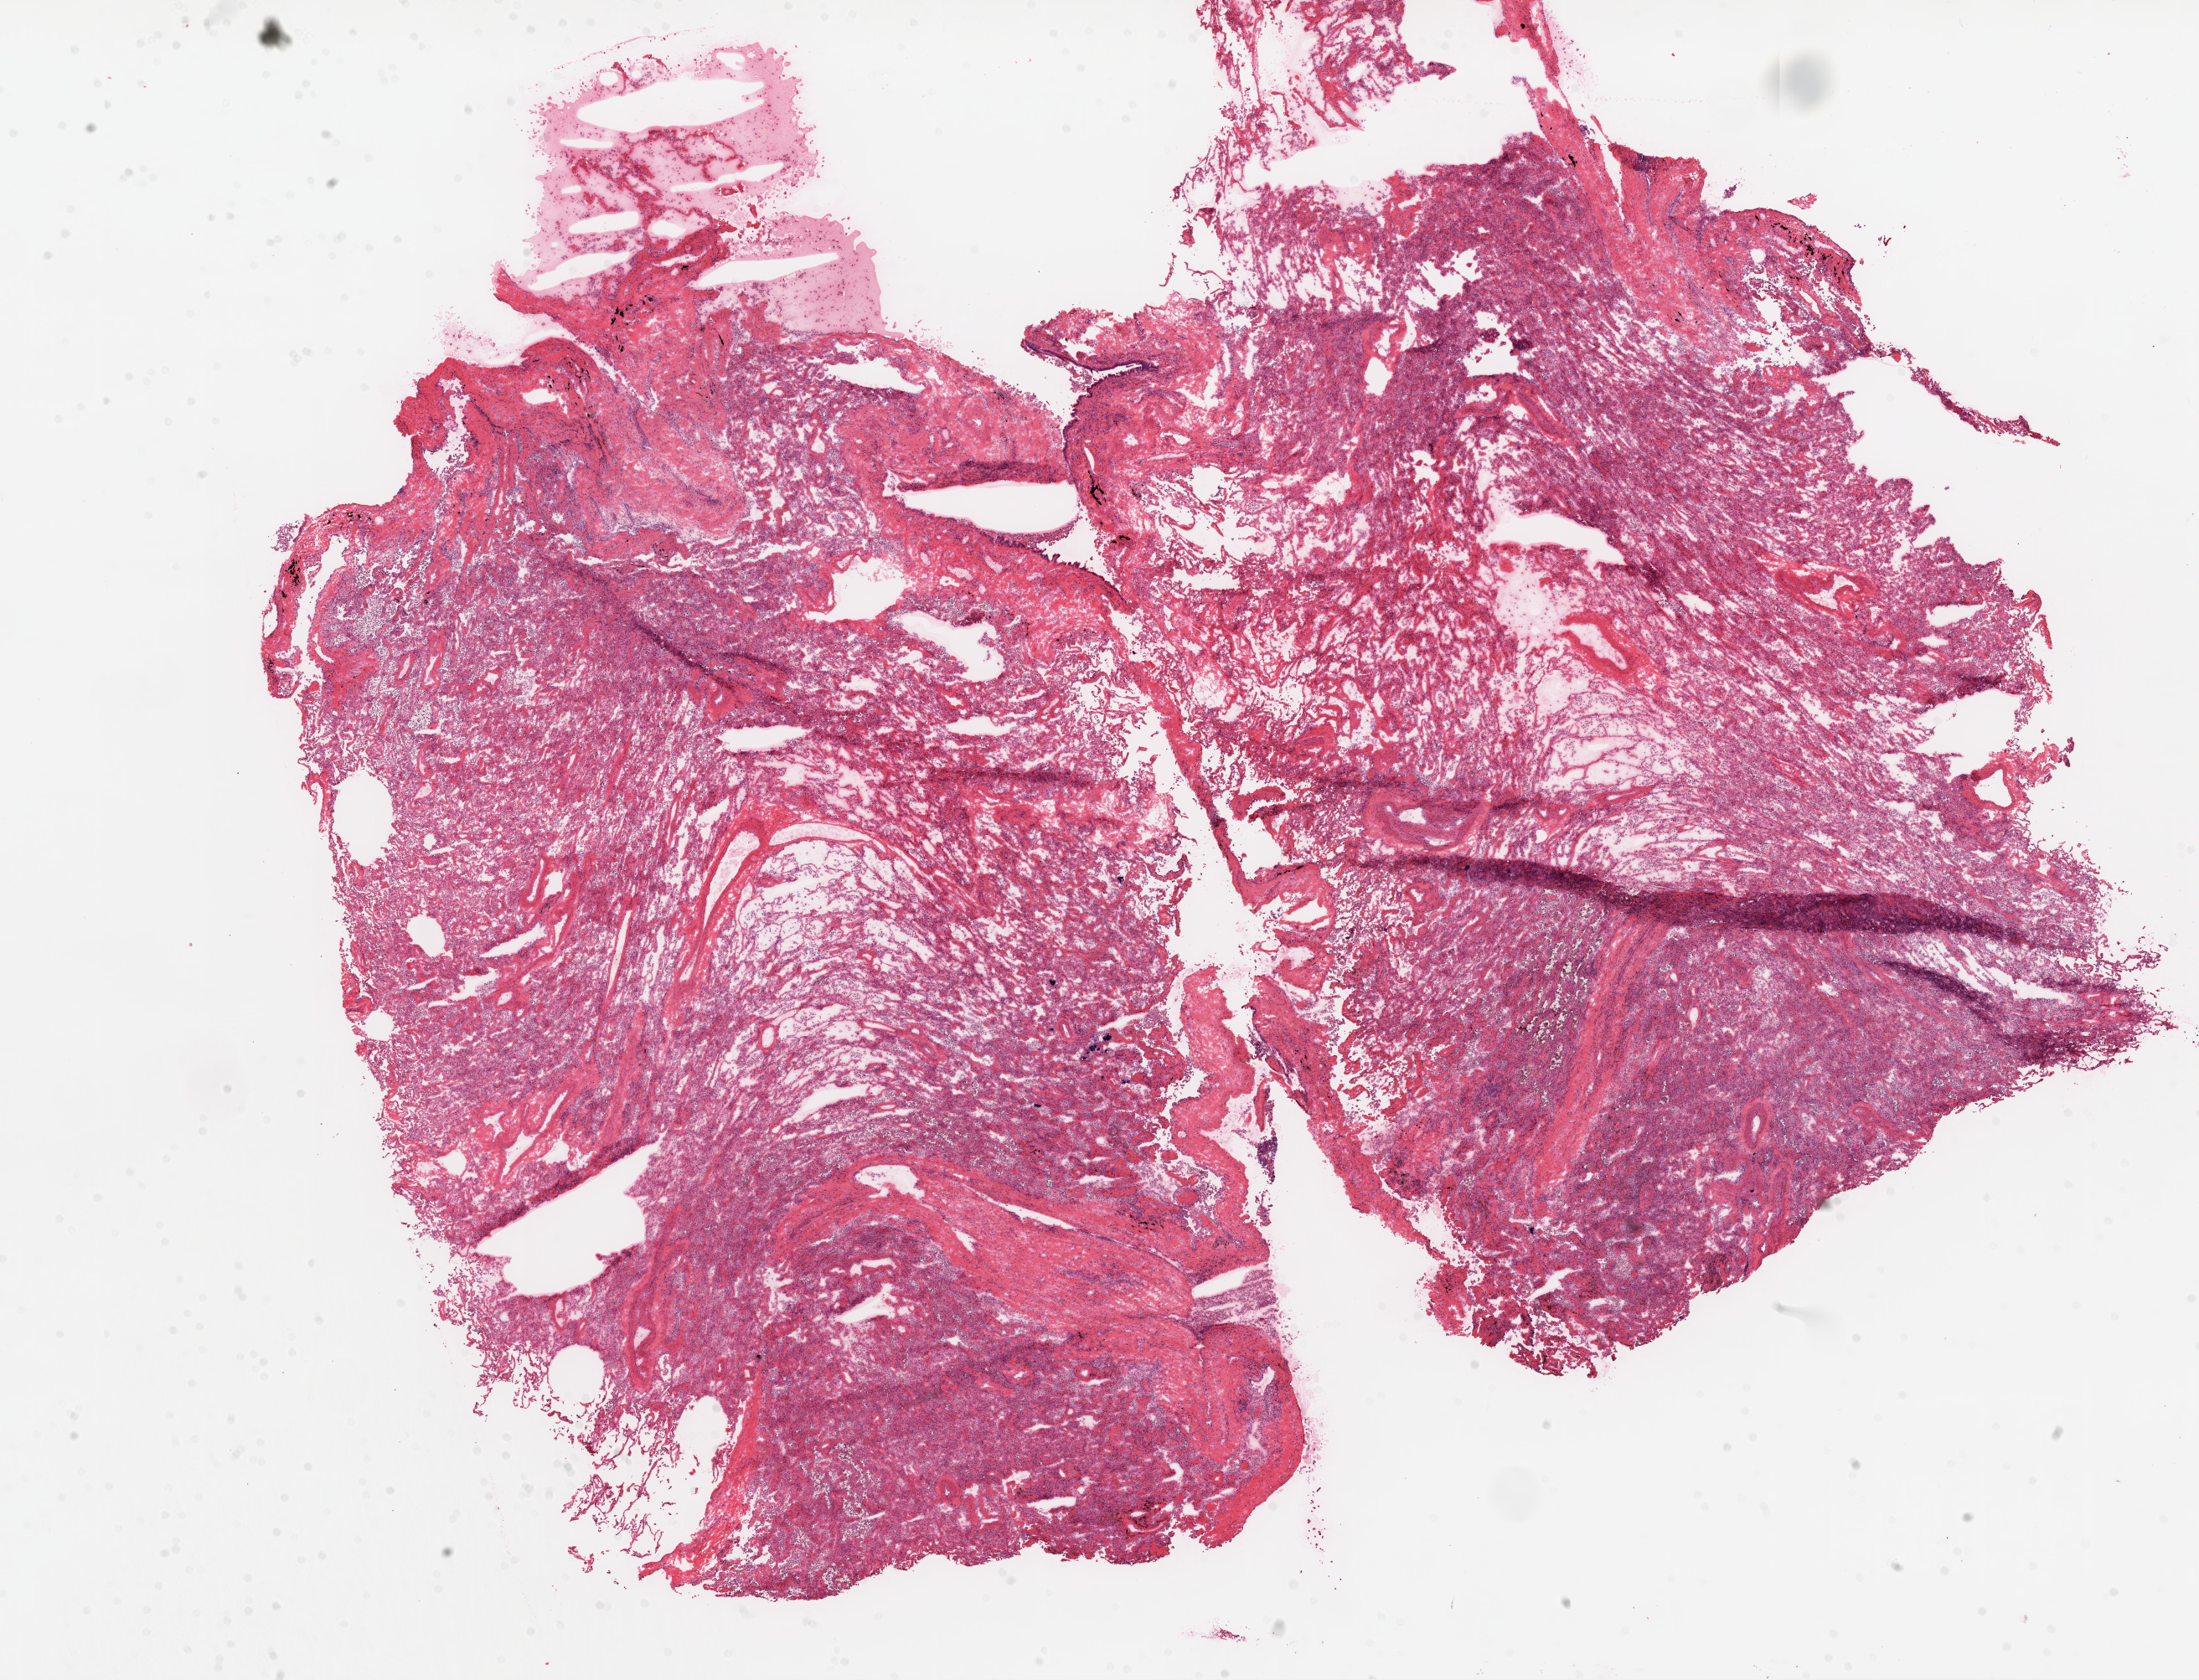
Hematoxylin and eosin (H&E) stained whole-slide image, a low-resolution overview of the entire scanned area, about 21.1 x 16.1 mm (slide scanned at 20x), frozen section, solid tissue normal (non-tumour tissue) sample from the lung. Patient: male, age at initial diagnosis 44 years.
• this section: solid tissue normal (non-tumour) sample from the same patient
• patient diagnosis: Basaloid squamous cell carcinoma (lower lobe, lung)